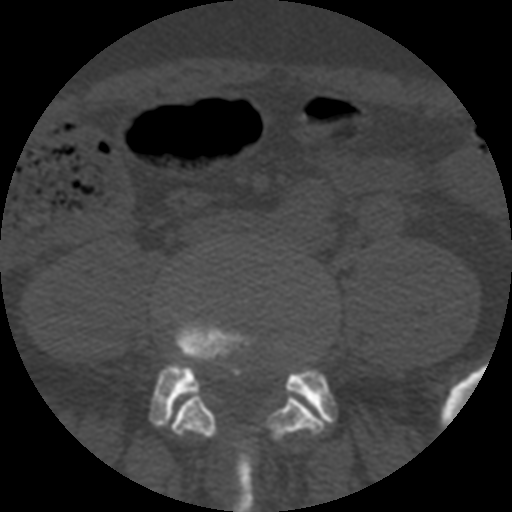
CT including the spine, one axial slice; slice 76 of 508 in the series (ordered by position); reconstruction kernel STANDARD; 120 kVp; bone window (W 1800 / L 400 HU); 1.25 mm slice thickness; 512 × 512 image matrix, field of view 160 × 160 mm. Patient age 57 years. Case-level facts recorded for this patient, not image findings: primary cancer: prostate.
Outlined on this slice (semi-automatic segmentation, software-assisted and operator-edited):
- L4 vertebra: bounding box (x1, y1, x2, y2) in pixels: (171, 390, 326, 447)
- L5 vertebra: (150, 325, 336, 512)